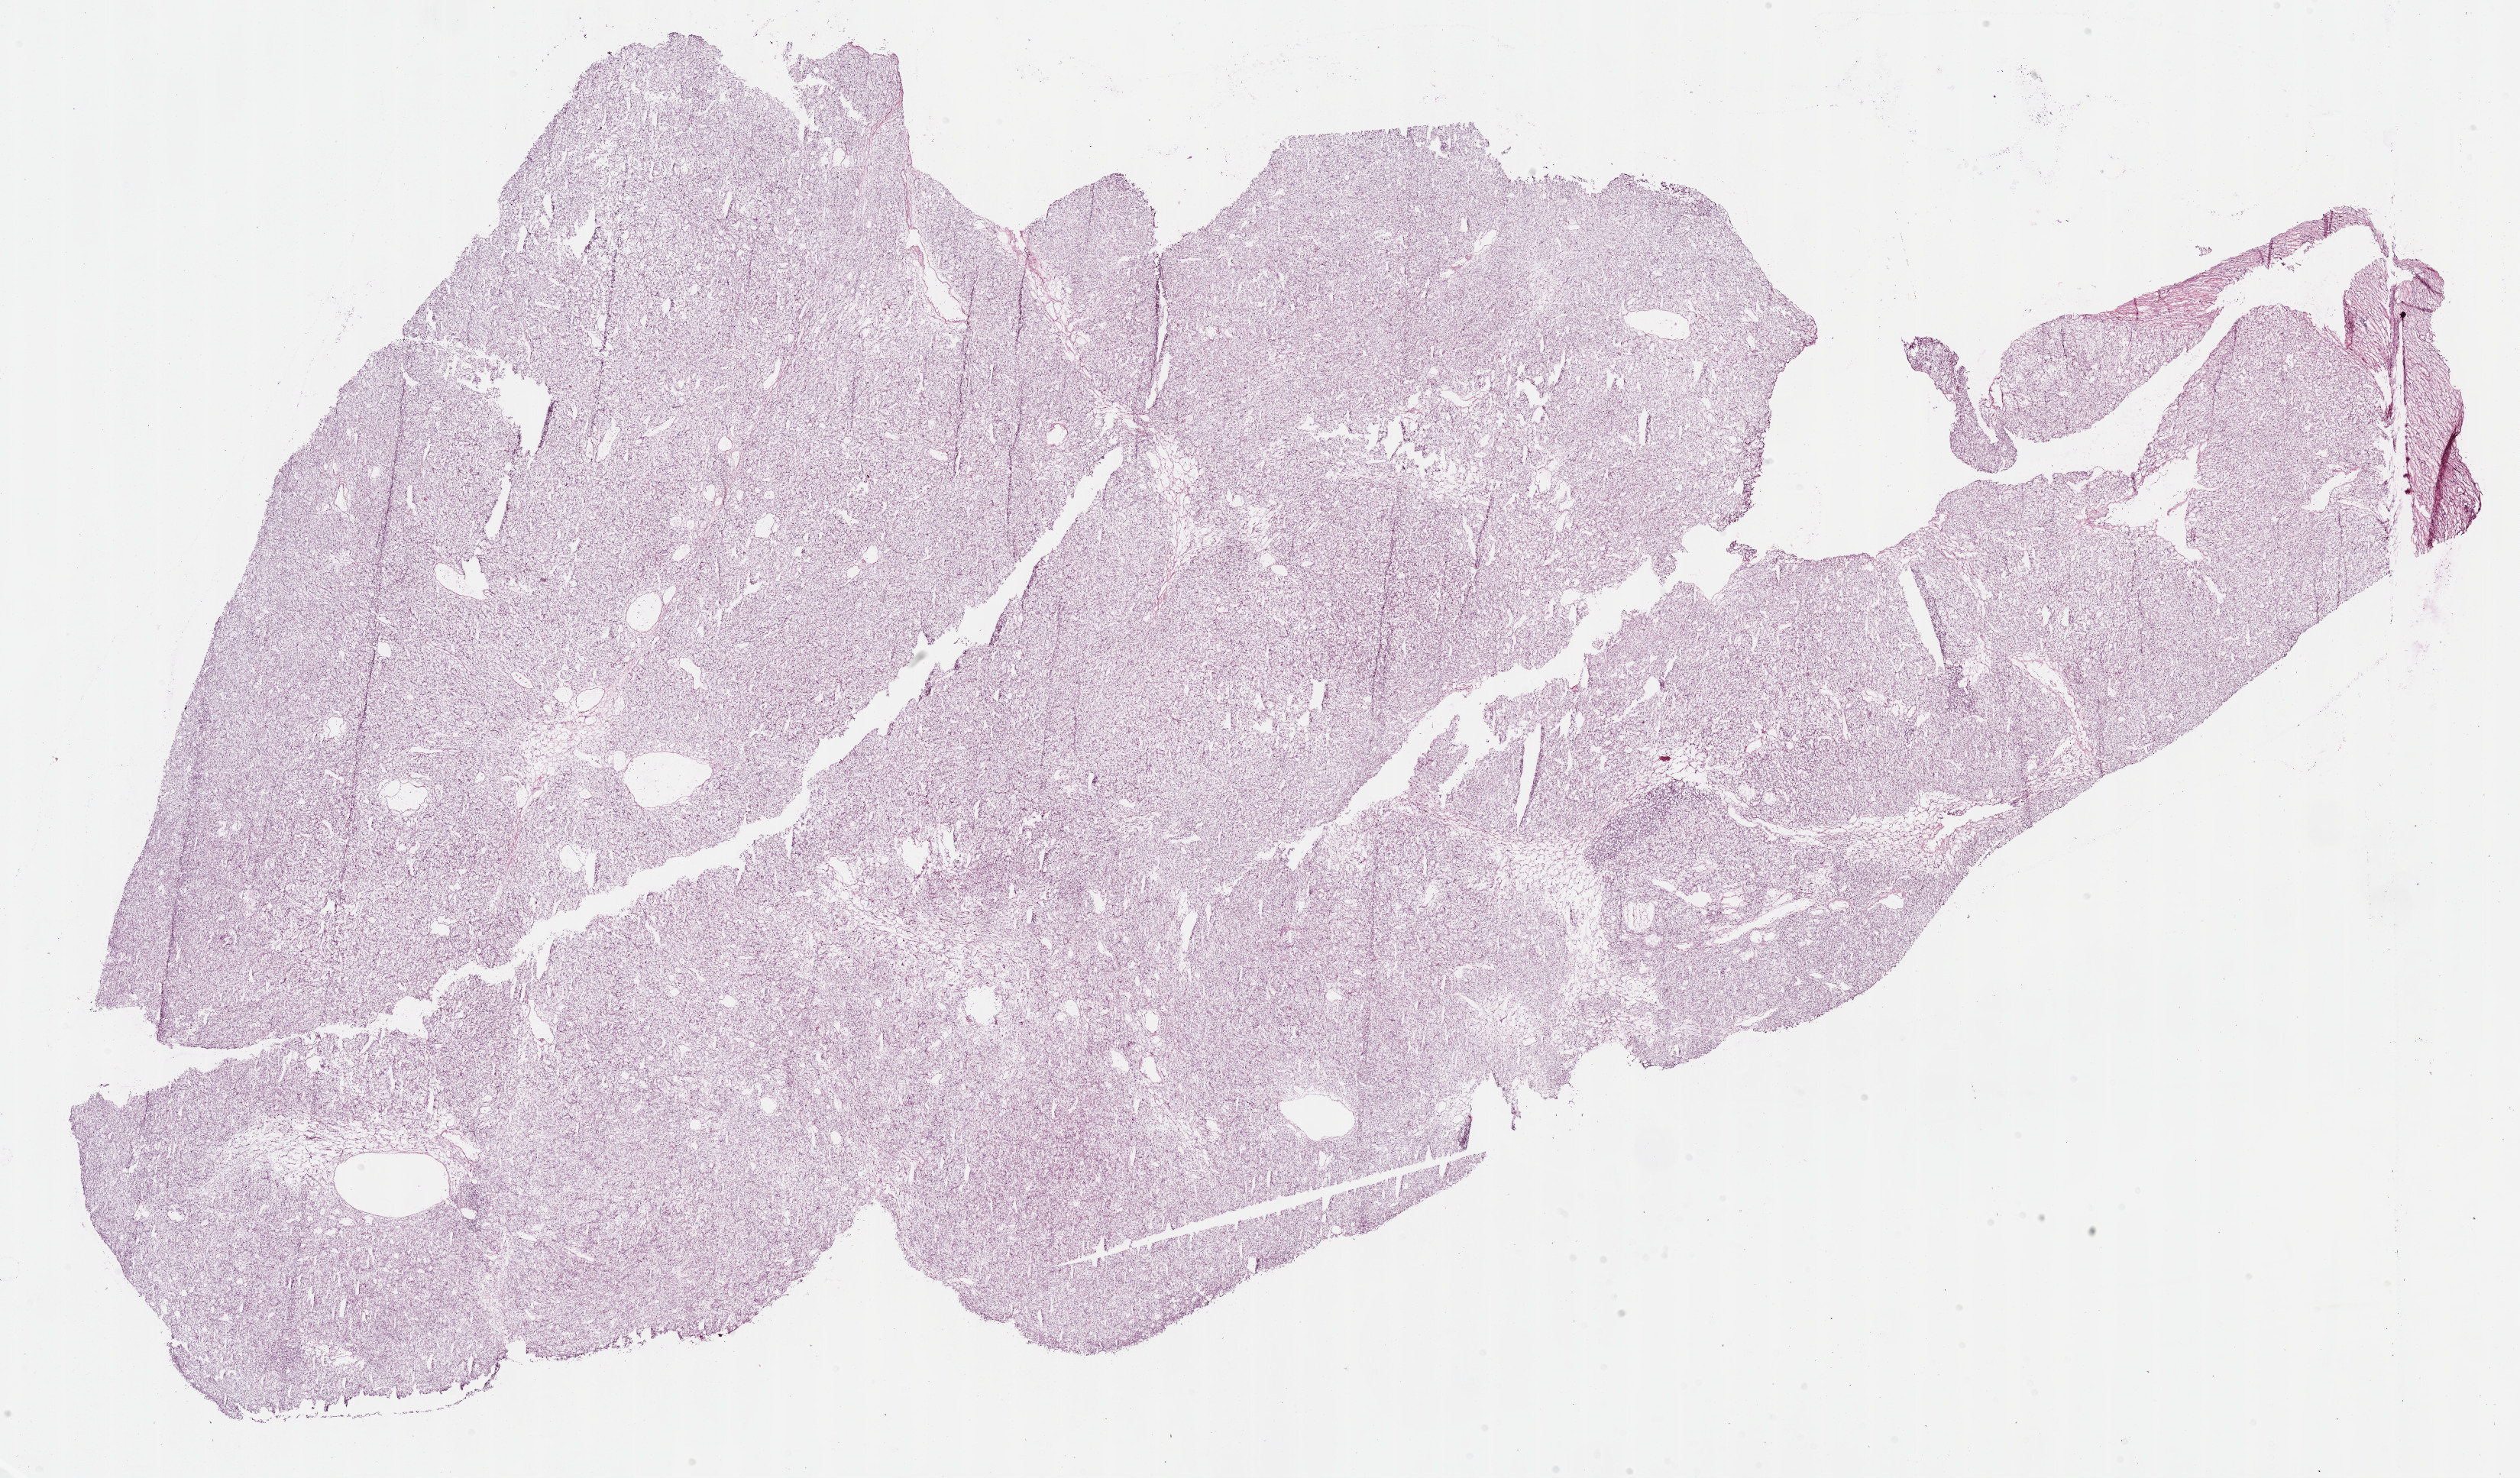
Digitized H&E tissue section (whole slide) — a low-resolution overview of the entire scanned area, about 26.7 x 15.6 mm. Frozen section from the bottom of the tissue portion. Kidney, primary tumour sample. Patient: male, age at initial diagnosis 61 years. Histologic grade: G4 (undifferentiated). Composition of this section per pathologist review: tumour cells 95%, tumour nuclei 90%, normal cells 0%, stromal cells 5%, necrosis 0%.
AJCC pathologic stage: III. Diagnosis: Clear cell adenocarcinoma, NOS. TNM: T3a NX M0.